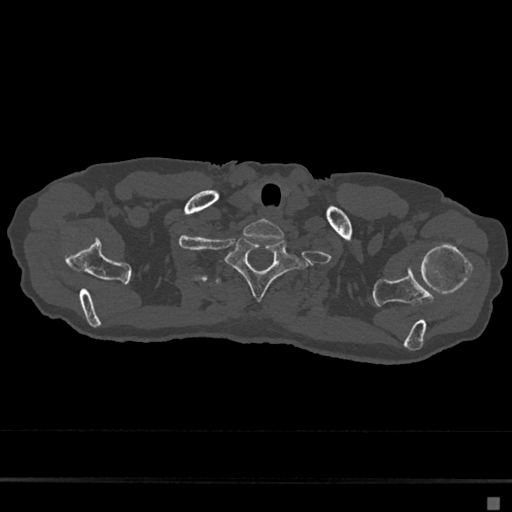
CT including the spine, one axial slice. Position 609 of 797 along the scan axis. Reconstruction kernel Br40s/3. 120 kVp. Bone window (W 1800 / L 400 HU). 0.5 mm slice thickness. 512 × 512 image matrix, field of view 360 × 360 mm. Patient: female, 68 years. Case-level facts recorded for this patient, not image findings: primary cancer: renal.
Outlined on this slice (semi-automatically segmented with operator editing):
- T1 vertebra: bounding box (x1, y1, x2, y2) in pixels: (225, 236, 299, 300)
- T2 vertebra: (215, 277, 222, 286)